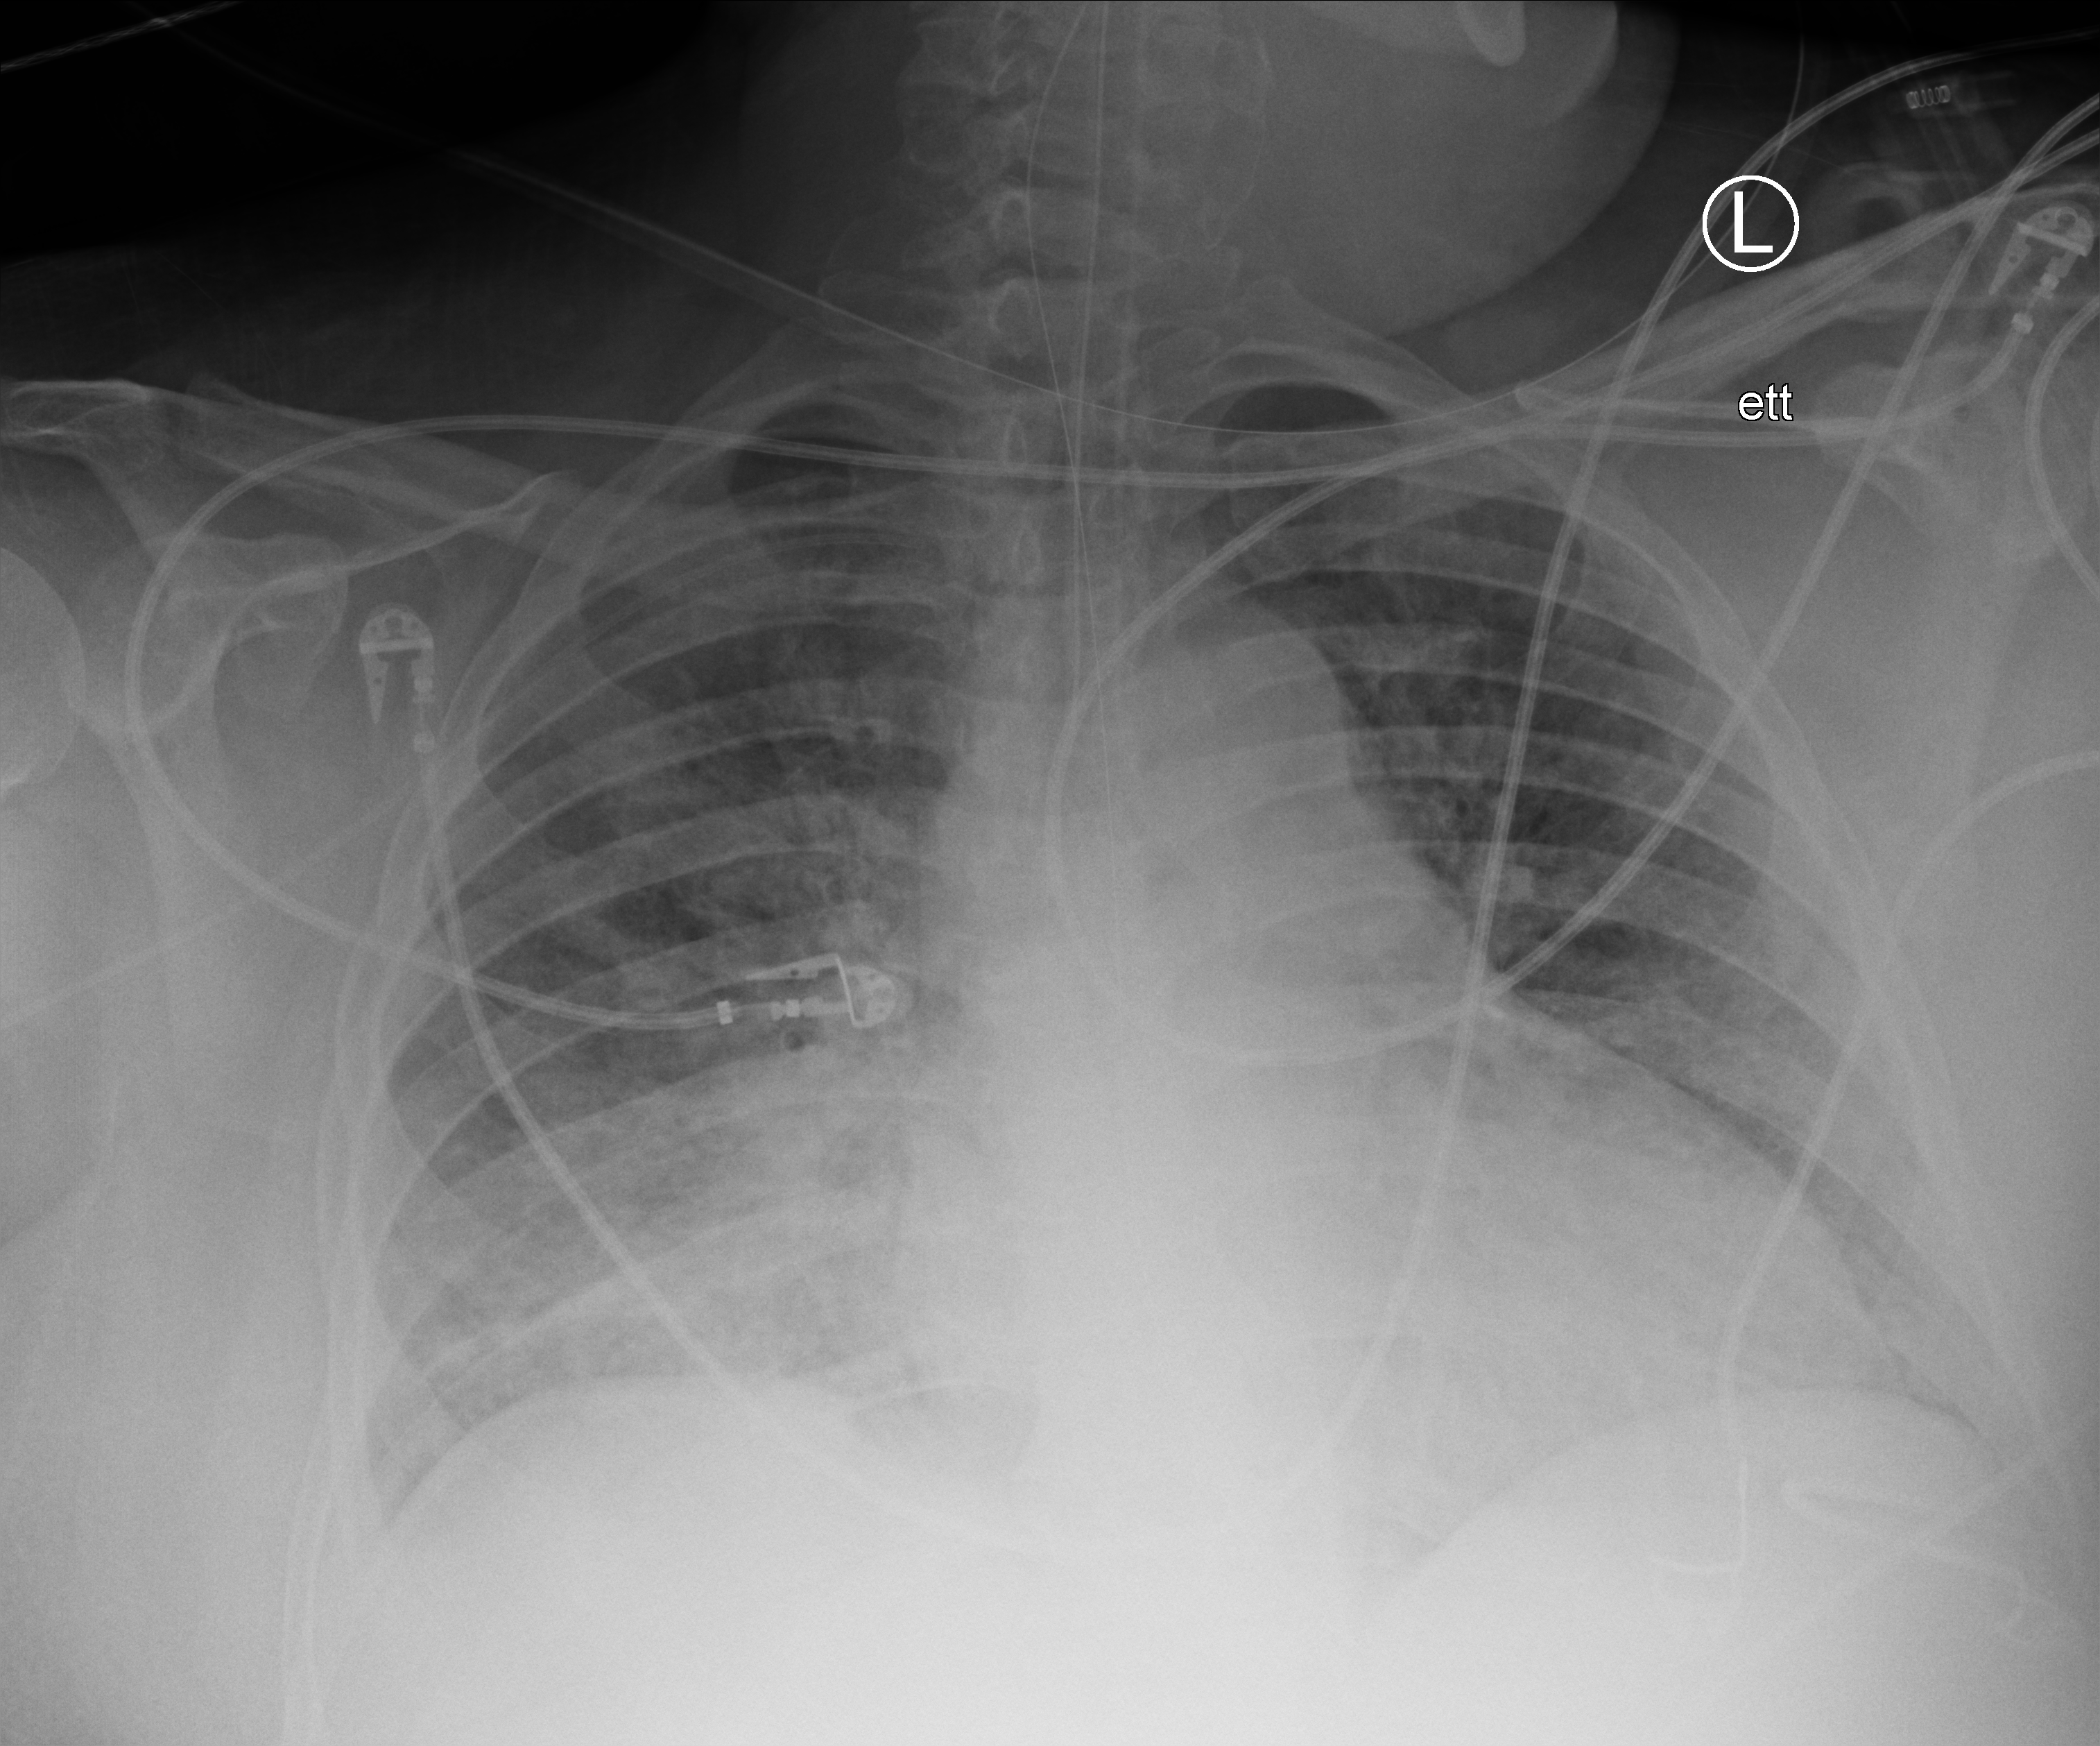
Bedside chest radiograph (computed radiography). Male patient hospitalised with COVID-19, age 18–59 years.
Hospital-stay facts (about this admission, not read from this image; timing relative to this image not recorded): admitted to intensive care during this hospital stay: yes; other chronic lung disease (admission record): no; diabetes (admission record): yes.